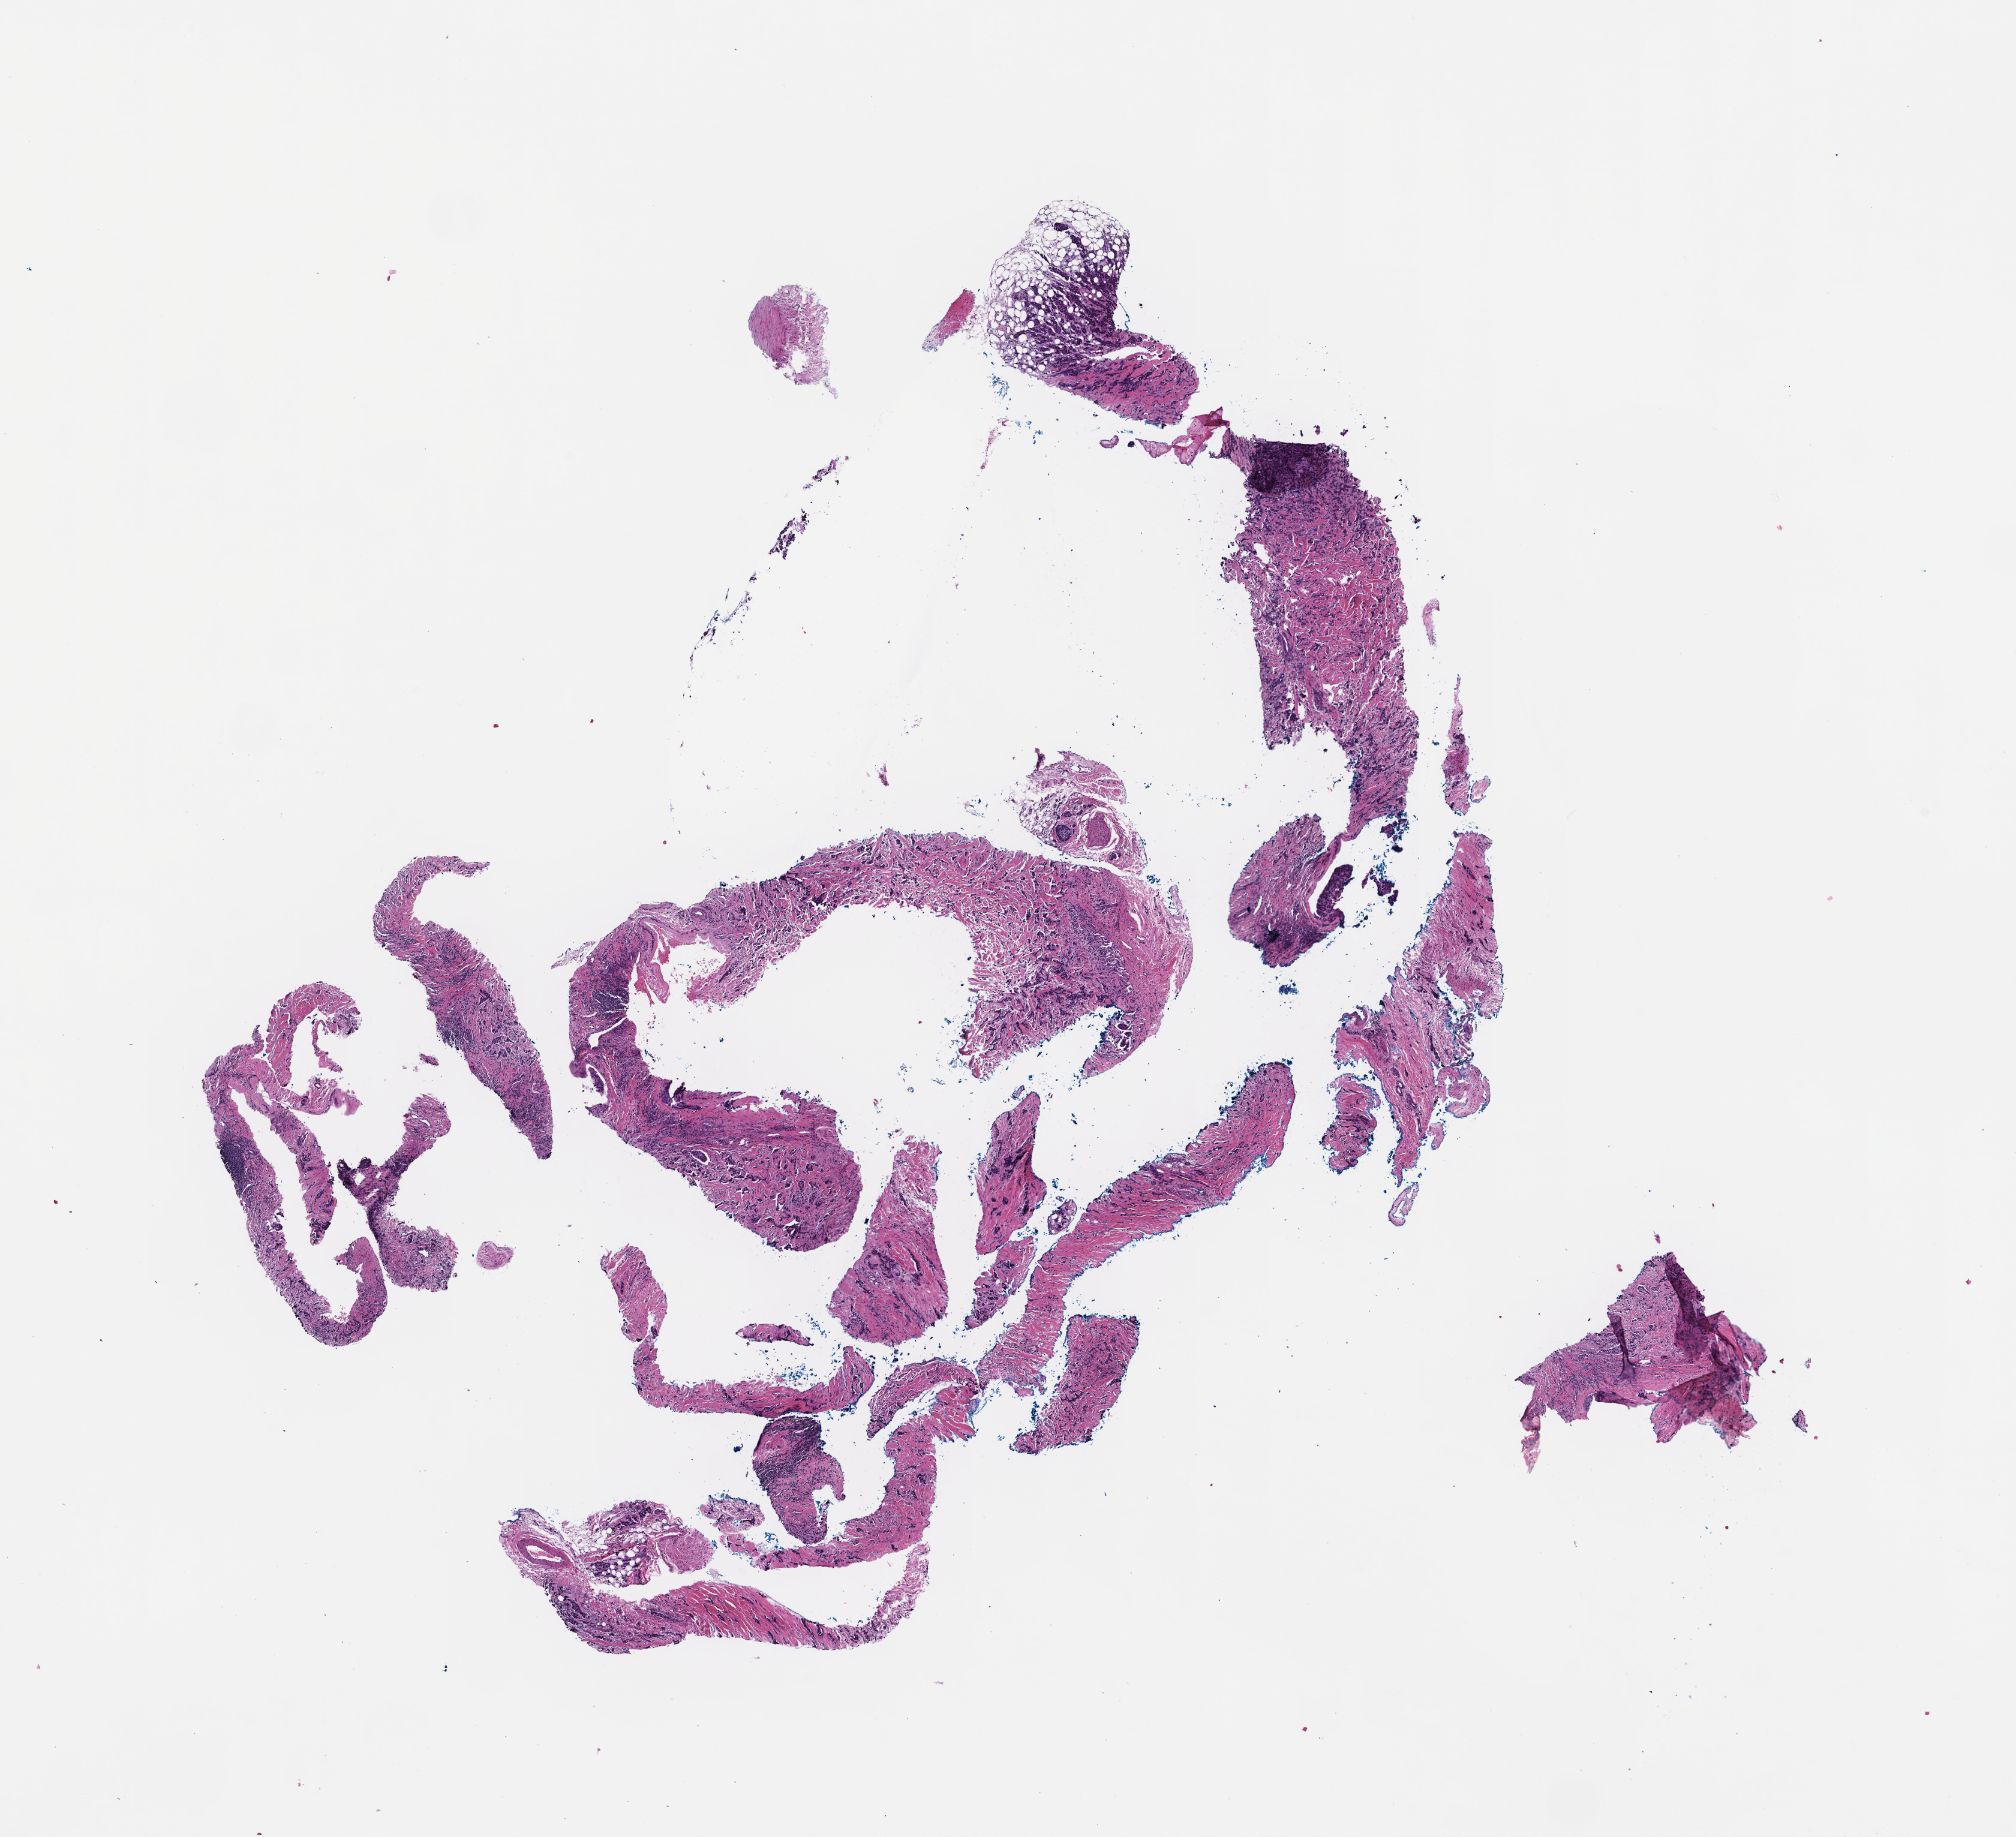
Digitized H&E-stained section — whole scanned area (about 13.6 x 12.4 mm) shown as a low-resolution overview; formalin-fixed paraffin-embedded section. Patient: female.
- this section: metastasis (sampled organ not recorded)
- primary diagnosis of the patient: Invasive Breast Carcinoma